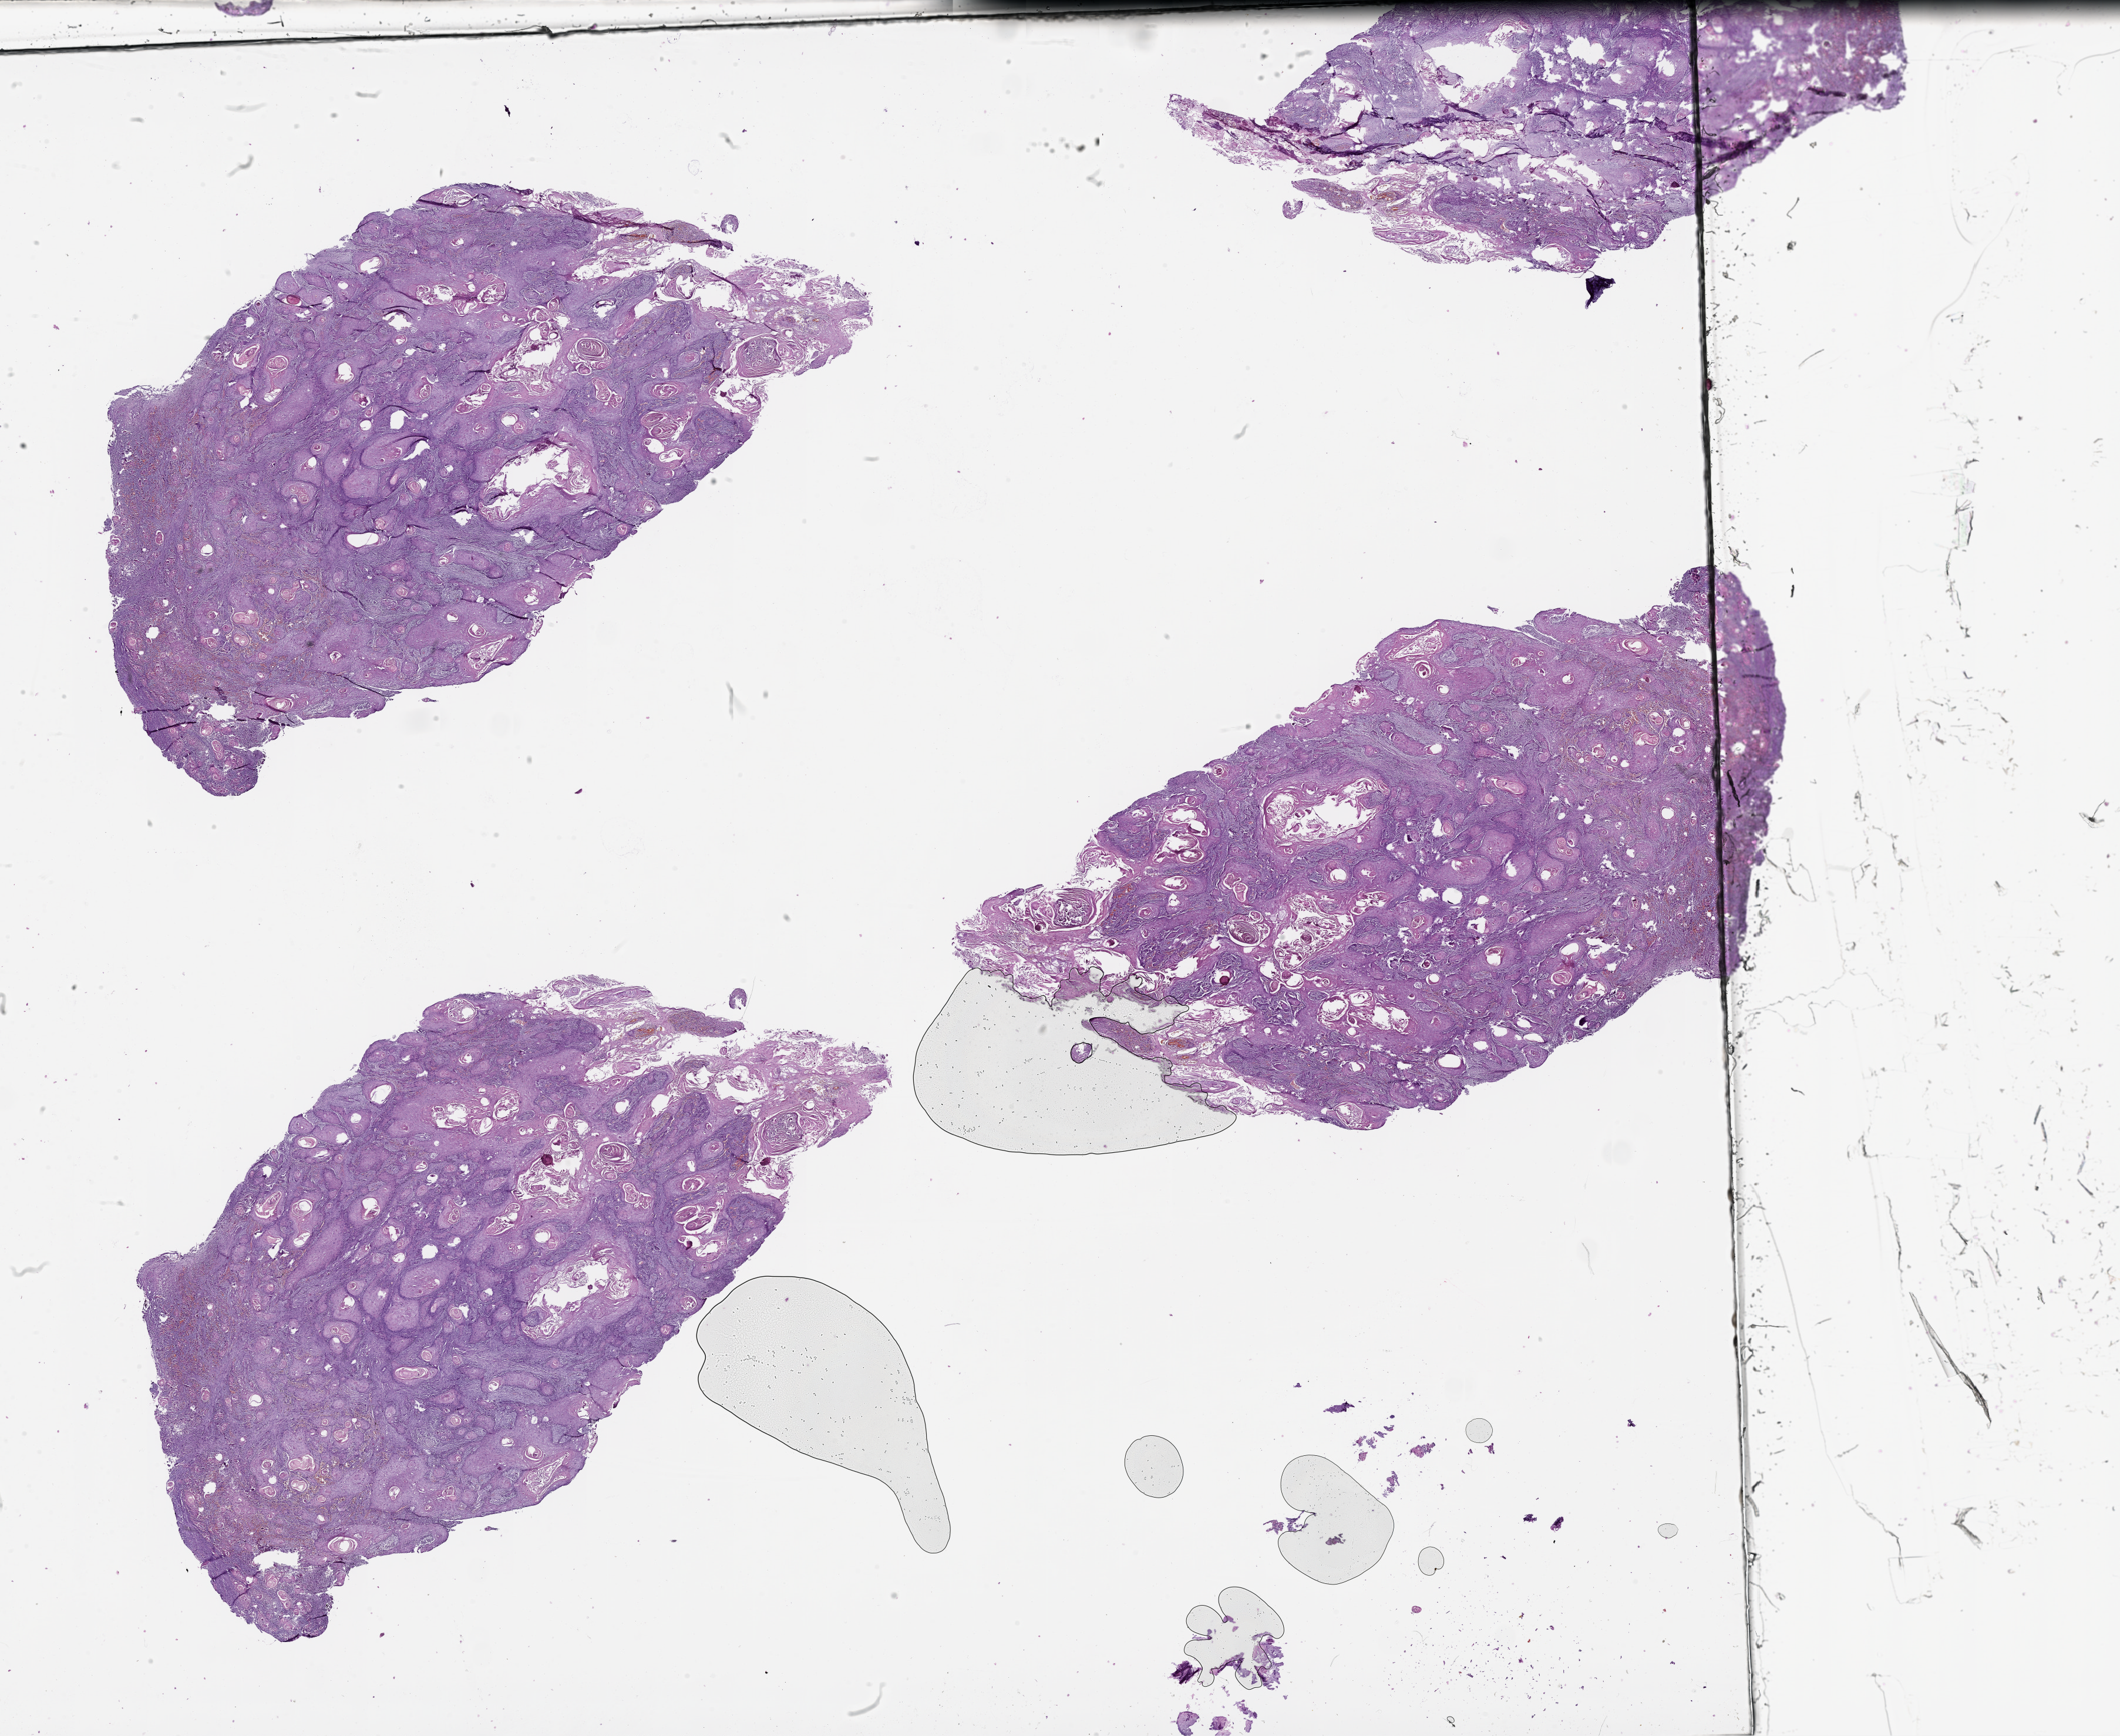
Whole-slide histology image, H&E, whole scanned area (about 29.1 x 23.8 mm) shown as a low-resolution overview, head and neck, tissue type not recorded.
Patient diagnosis (cohort enrolment): head and neck cancer (head-neck).